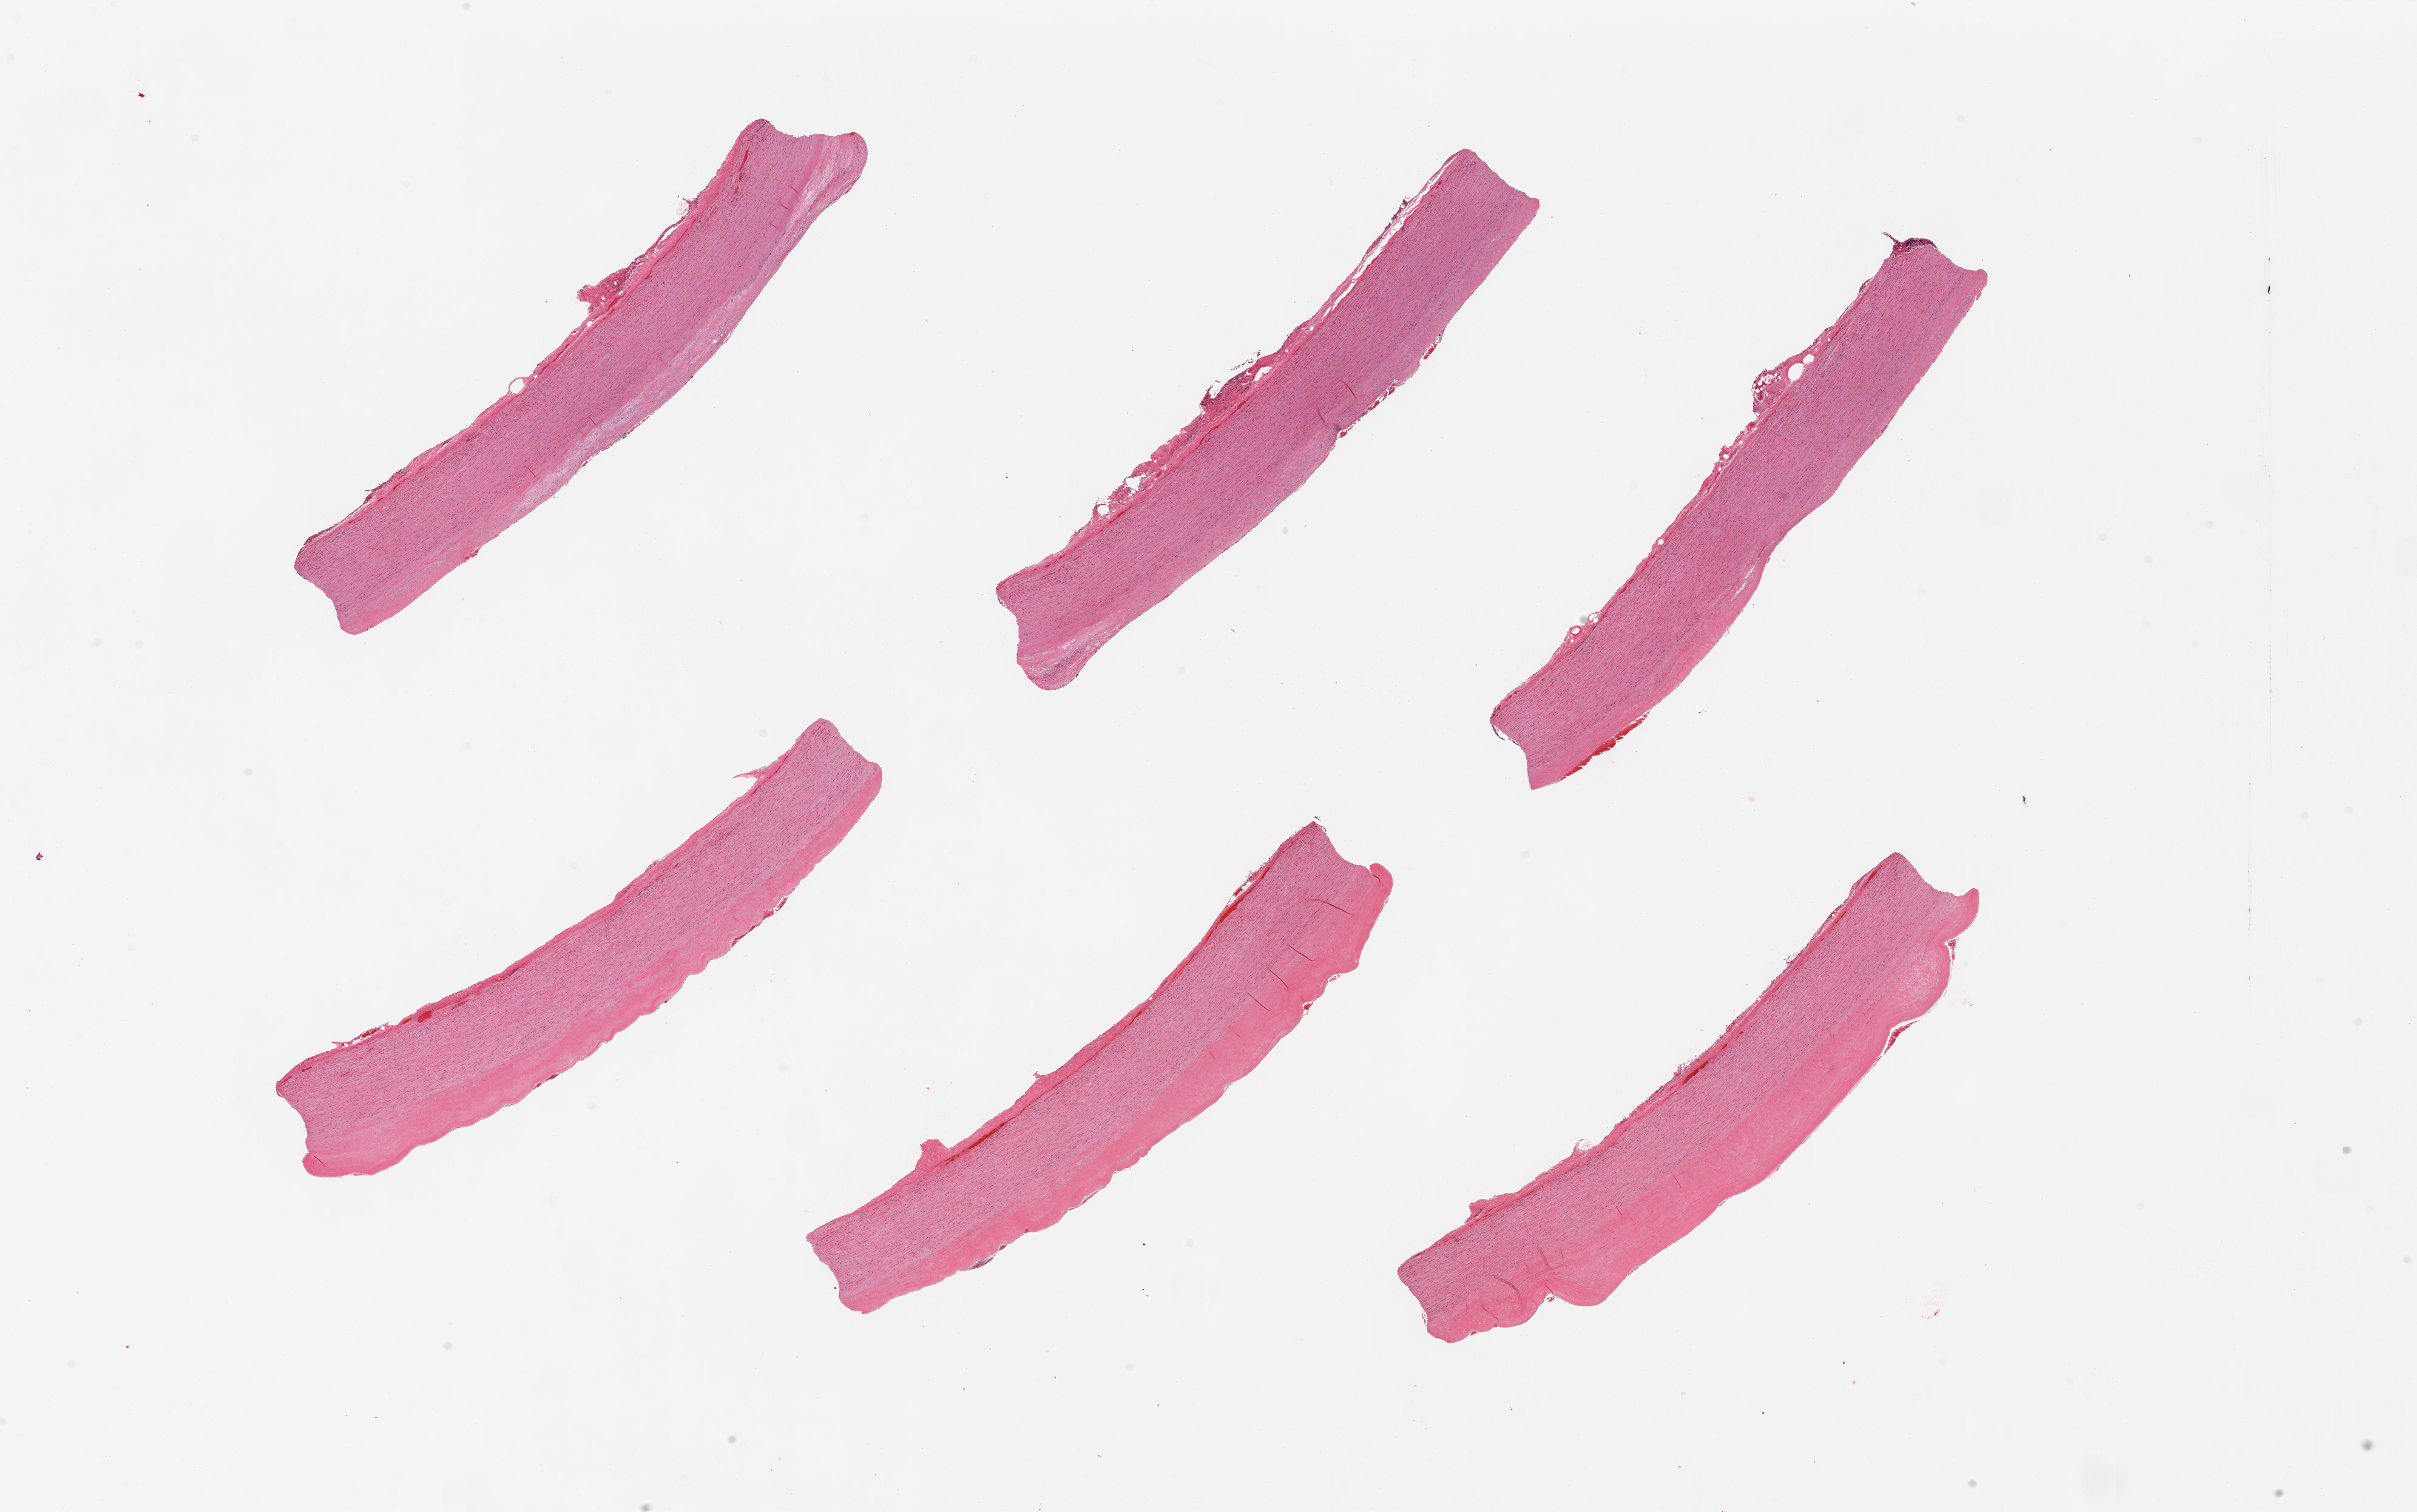
Haematoxylin and eosin whole-slide image — whole scanned area (about 31.5 x 19.7 mm, from a 20x scan) shown as a low-resolution overview; PAXgene-fixed, paraffin-embedded tissue; section of aorta (target tissue); donor tissue sample. Donor: male.
* reviewer comment on this tissue sample: 6 pieces; fibrous/sclerotic plaque formation; well trimmed